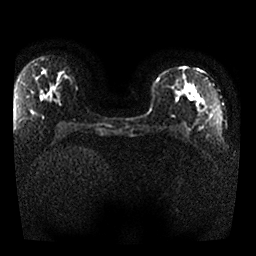
Breast MRI, one axial slice. Position 16 of 25 along the scan axis. Diffusion-weighted series; image 2 of 4 stored at this slice position (different b-values; order by instance number). 1.5 T. 4 mm slice thickness. 256 × 256 image matrix. Female patient.
Structures marked on this image (outlined manually by an expert reader):
- tumour on diffusion-weighted imaging: bounding box (x1, y1, x2, y2) in pixels: (174, 88, 194, 102)